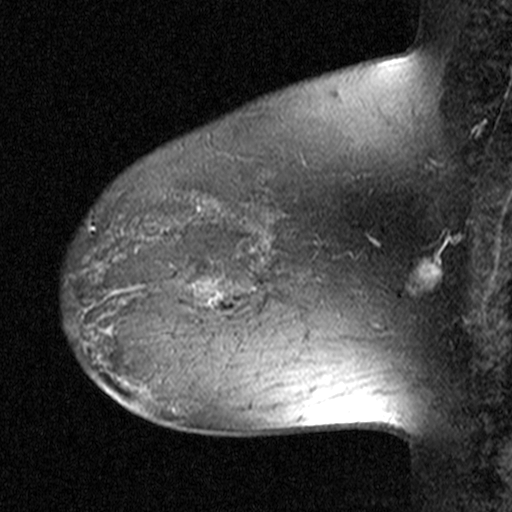
Breast MRI (dynamic contrast-enhanced), one sagittal slice. Slice 32 of 44 in the series (ordered by position). Dynamic contrast-enhanced study with each time point stored as its own series, time point 2 of 3 at this slice position (early post-contrast, ordered by acquisition time). 1.5 T. TE 4.5 ms, TR 11 ms. 3 mm slice thickness. 512 × 512 image matrix, field of view 200 × 200 mm. Female patient, age 38 years. Case-level facts recorded for this patient, not image findings: setting: breast cancer imaged before/during neoadjuvant chemotherapy; receptor status: HR-positive, HER2-negative.
Outlined on this slice (semi-automatically segmented with operator editing):
- analysis volume of interest (the breast-tissue region the enhancement analysis was run in; not a lesion): bounding box [x1, y1, x2, y2] px = [152, 236, 253, 335]
- tumour enhancement mask (voxels above the 90 % enhancement threshold inside the analysis volume of interest): [193, 248, 253, 308]